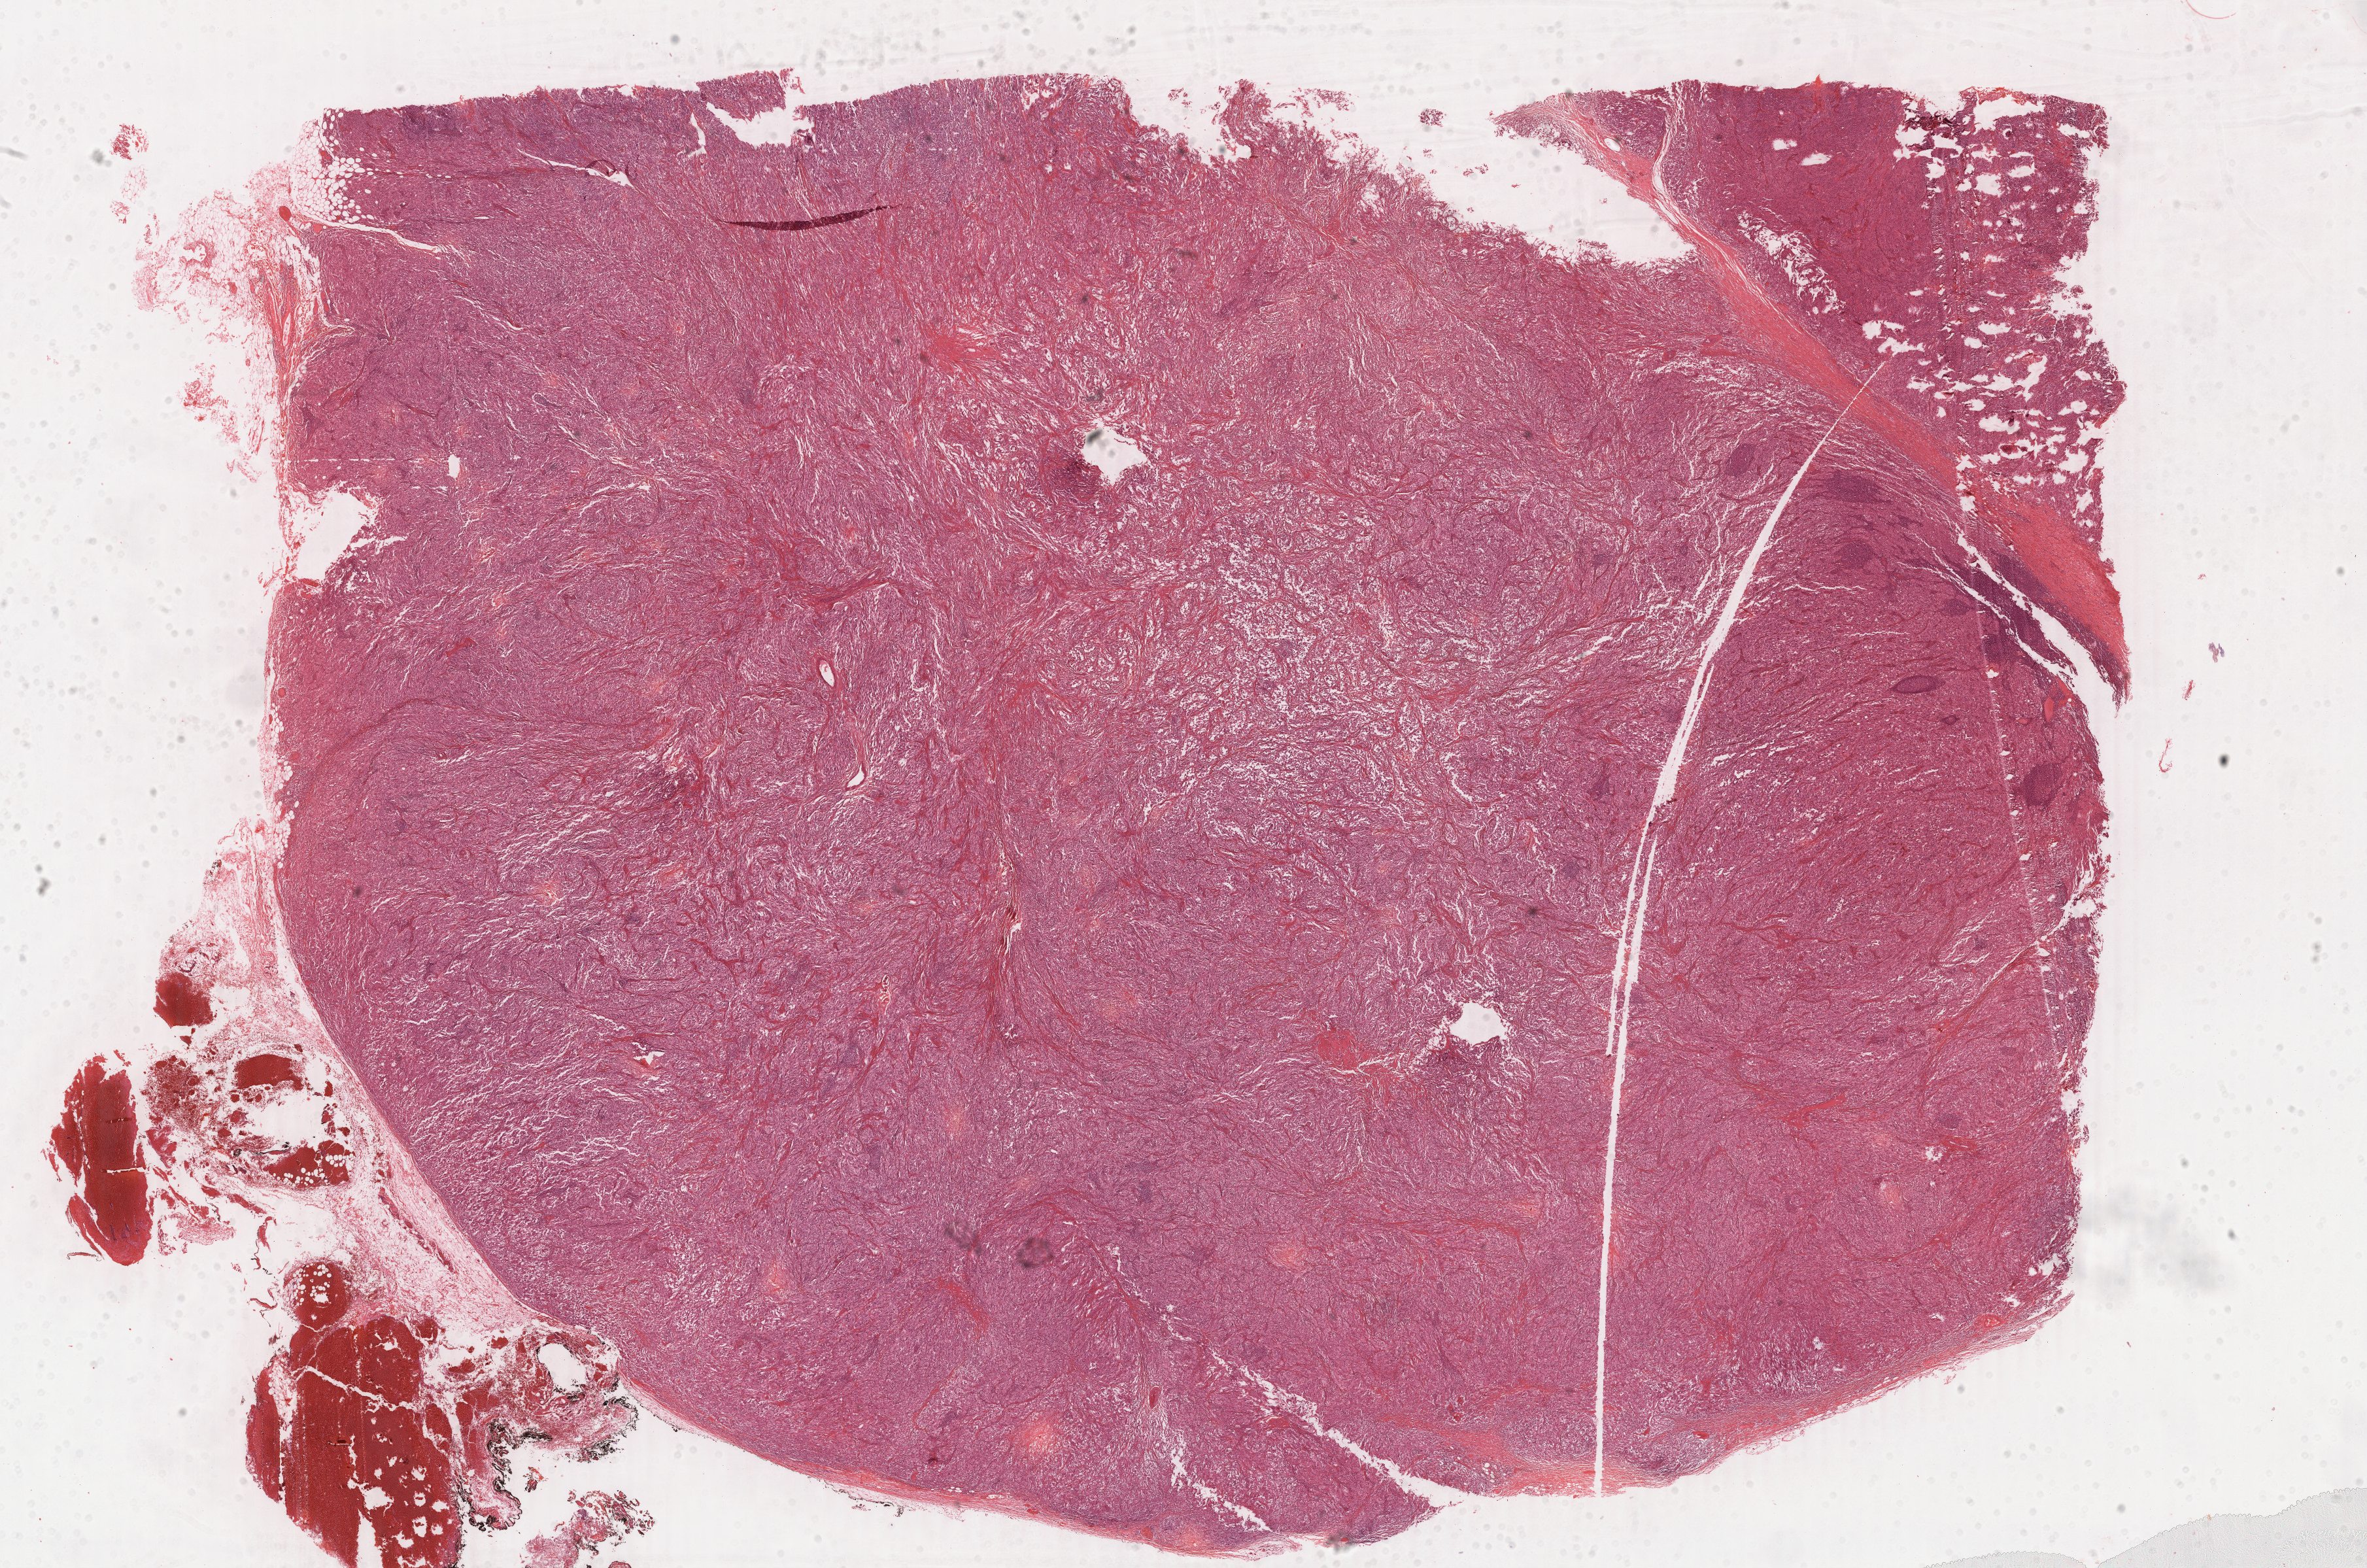
Digitized H&E-stained tissue section (whole slide), whole scanned area (about 28.8 x 19.1 mm) shown as a low-resolution overview, FFPE section, sample: primary tumour, skin. Male, age 62 years at initial diagnosis.
* pathologic diagnosis: Malignant melanoma, NOS